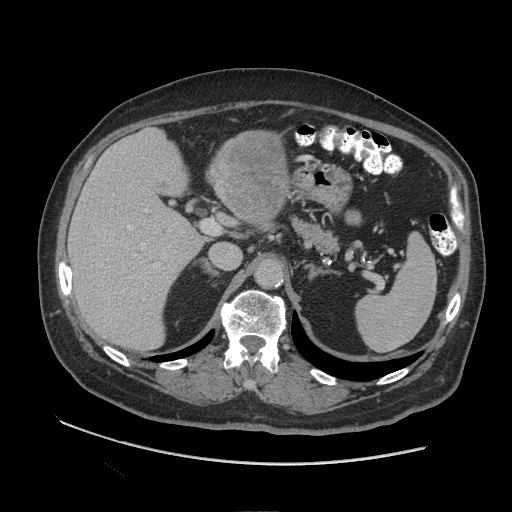
Contrast-enhanced abdominal CT (liver protocol), one axial slice; position 55 of 109 along the scan axis; 140 kVp; soft-tissue window (W 400 / L 40 HU); 2.5 mm slice thickness; 512 × 512 image matrix, field of view 420 × 420 mm. From the clinical record (not read from this slice): diagnosis: hepatocellular carcinoma (patient treated with transarterial chemoembolisation; whether this scan precedes or follows treatment is not stated here); TNM stage (as recorded): Stage-I; Child-Pugh class: A.
Outlined on this slice (semi-automatic segmentation, software-assisted and operator-edited):
- liver parenchyma outside the tumour (the mass and vessels are separate outlines, so this box may not span the whole liver): box from (x=68, y=129) to (x=227, y=350) px
- mass: (x=218, y=129)–(x=289, y=229)
- liver vessels: (x=108, y=208)–(x=161, y=268)